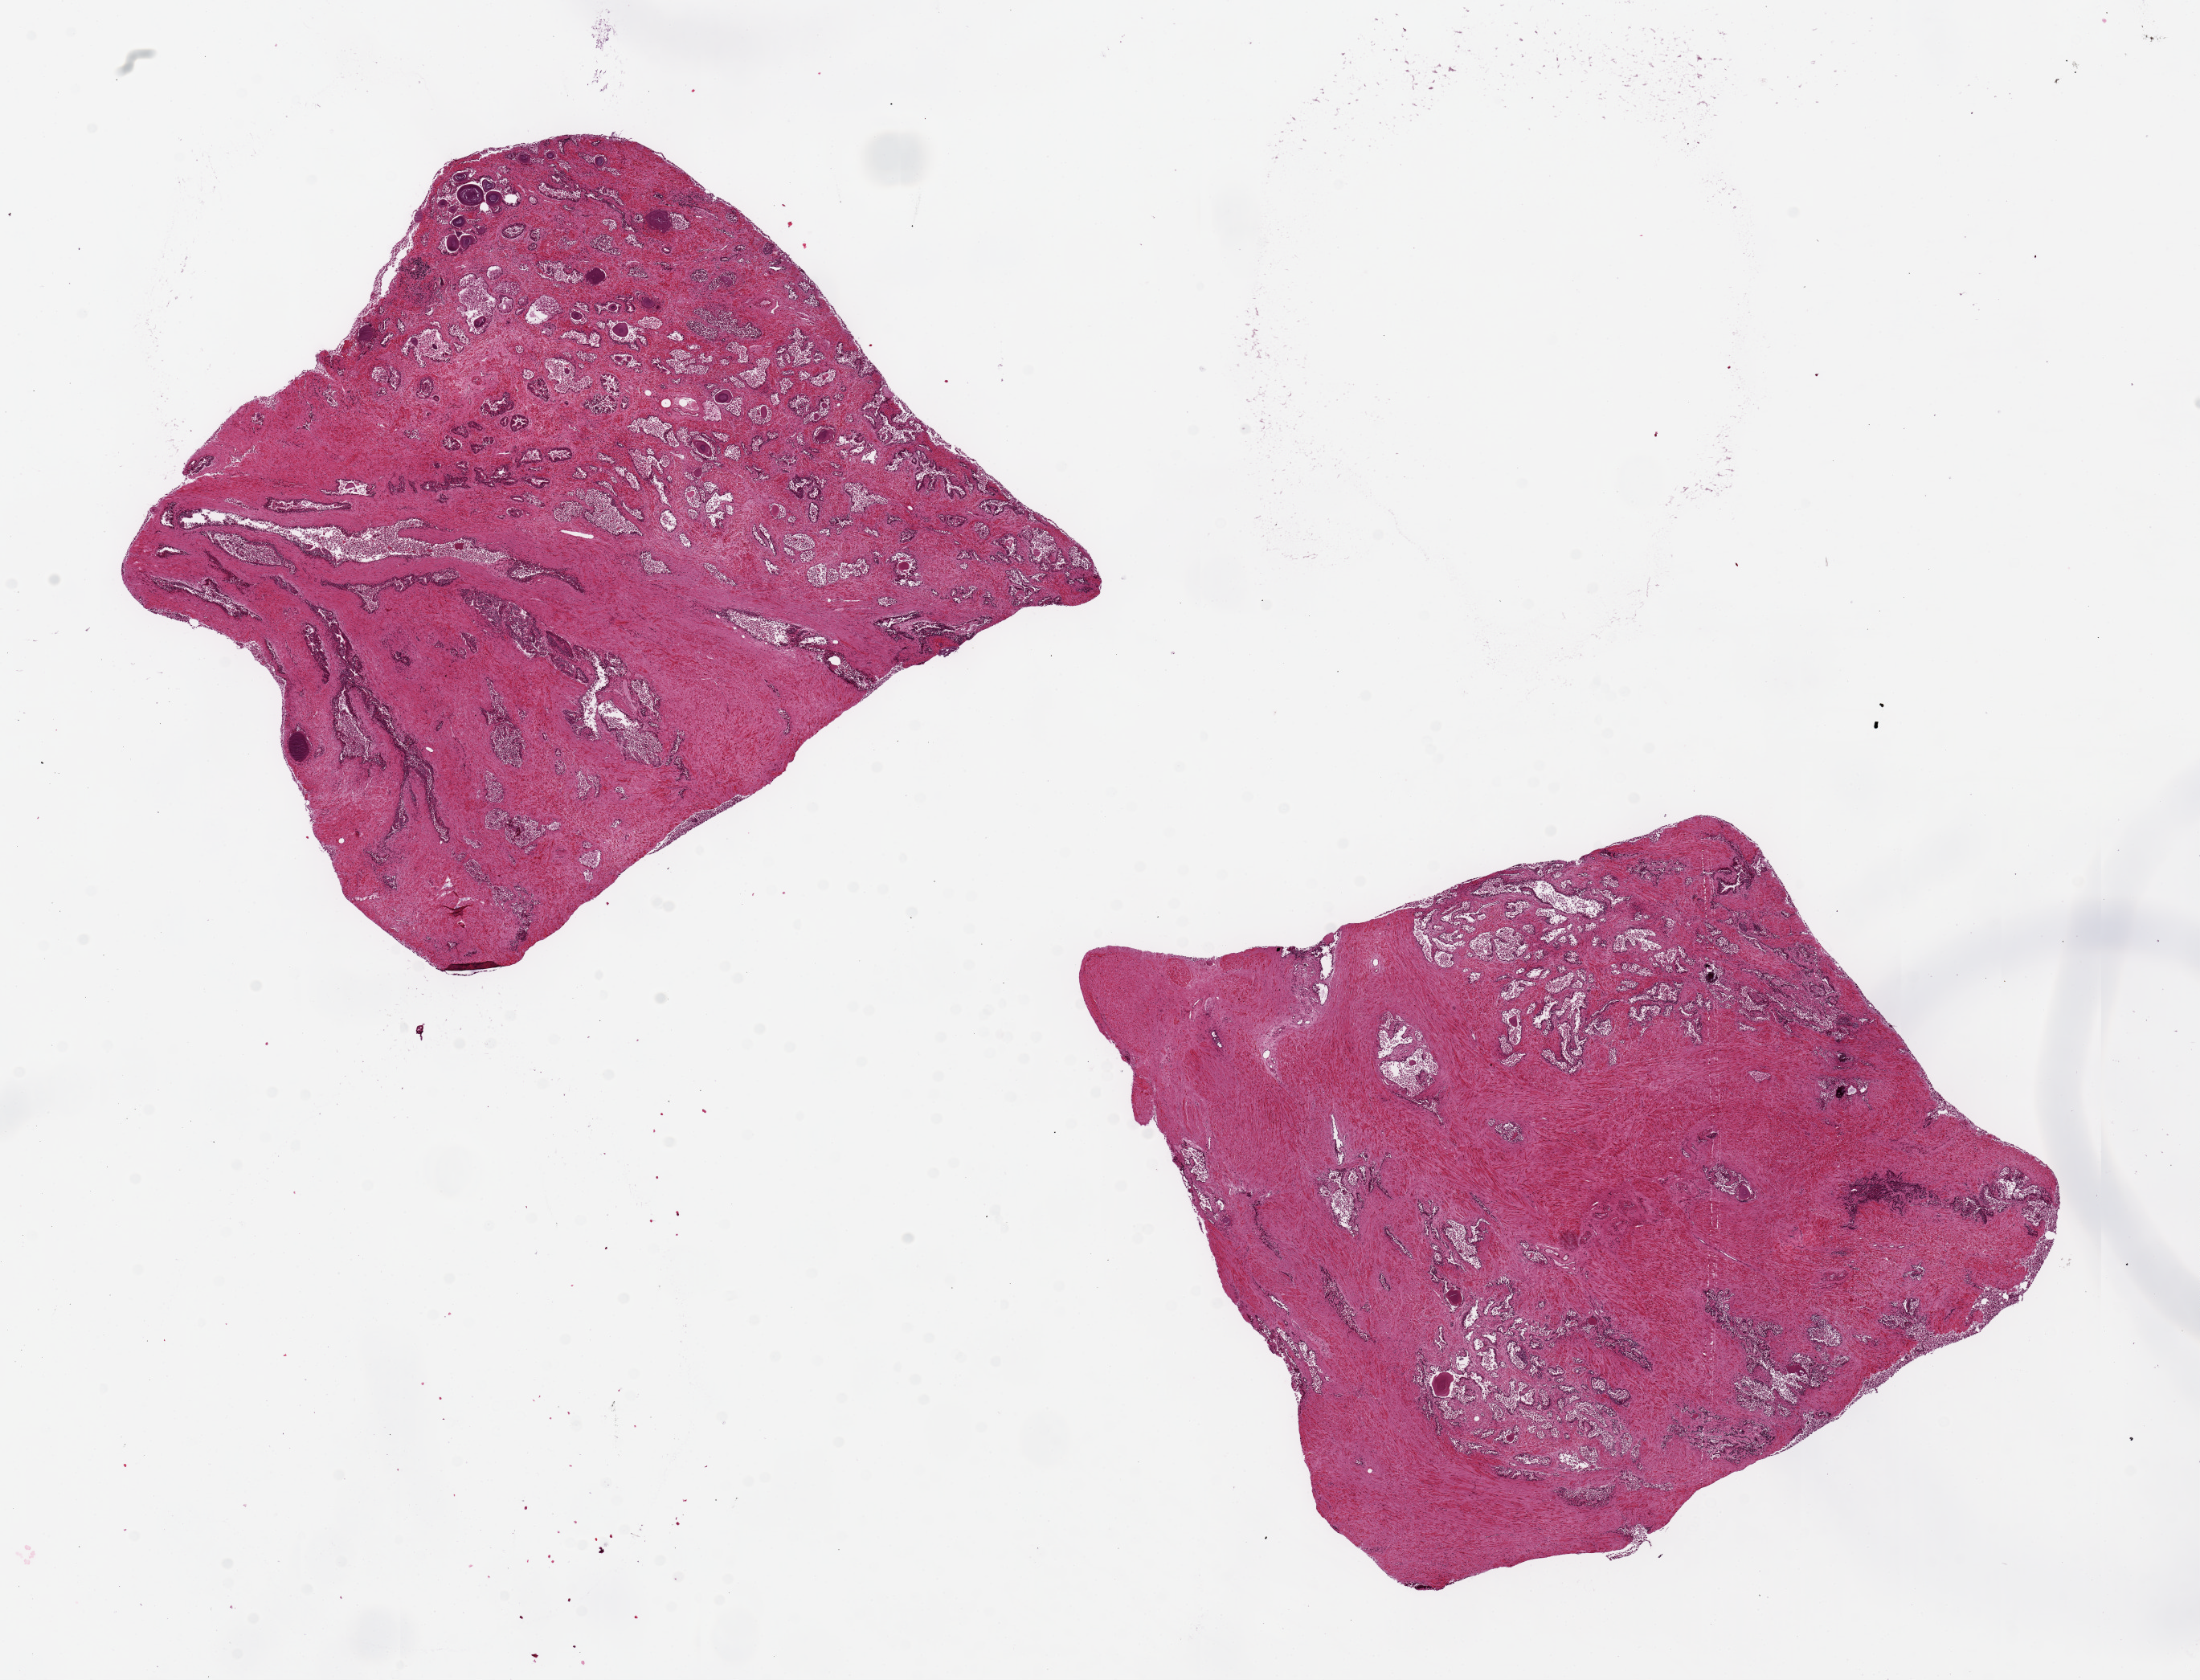
Digitized haematoxylin and eosin-stained section, brightfield — whole scanned area (about 21.7 x 16.5 mm, slide scanned at 20x) shown as a low-resolution overview; PAXgene-fixed paraffin-embedded (PFPE) section; section of prostate (target tissue); donor tissue sample. Male donor.
Pathologist's review note for this sample: 2 pieces, 7.5x7 & 8x8mm; Glands=3; fibromuscular stroma=1 (autolysis).